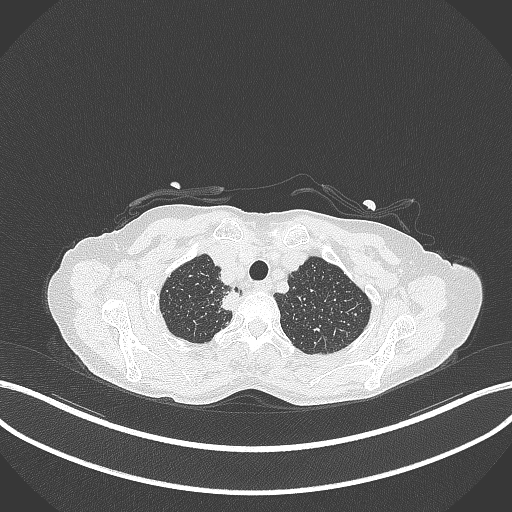
Chest CT, one axial slice. Position 329 of 403 along the scan axis. 120 kVp. Lung window (W 1500 / L -600 HU). 1 mm slice thickness. 512 × 512 image matrix. Patient: female, 75 years. From the clinical record (not read from this slice): clinical TNM (as recorded): T1c N1 M1.
Outlined on this slice (bounding box drawn by a radiologist):
- lung tumour (recorded histology: adenocarcinoma): box from (x=217, y=286) to (x=244, y=314) px